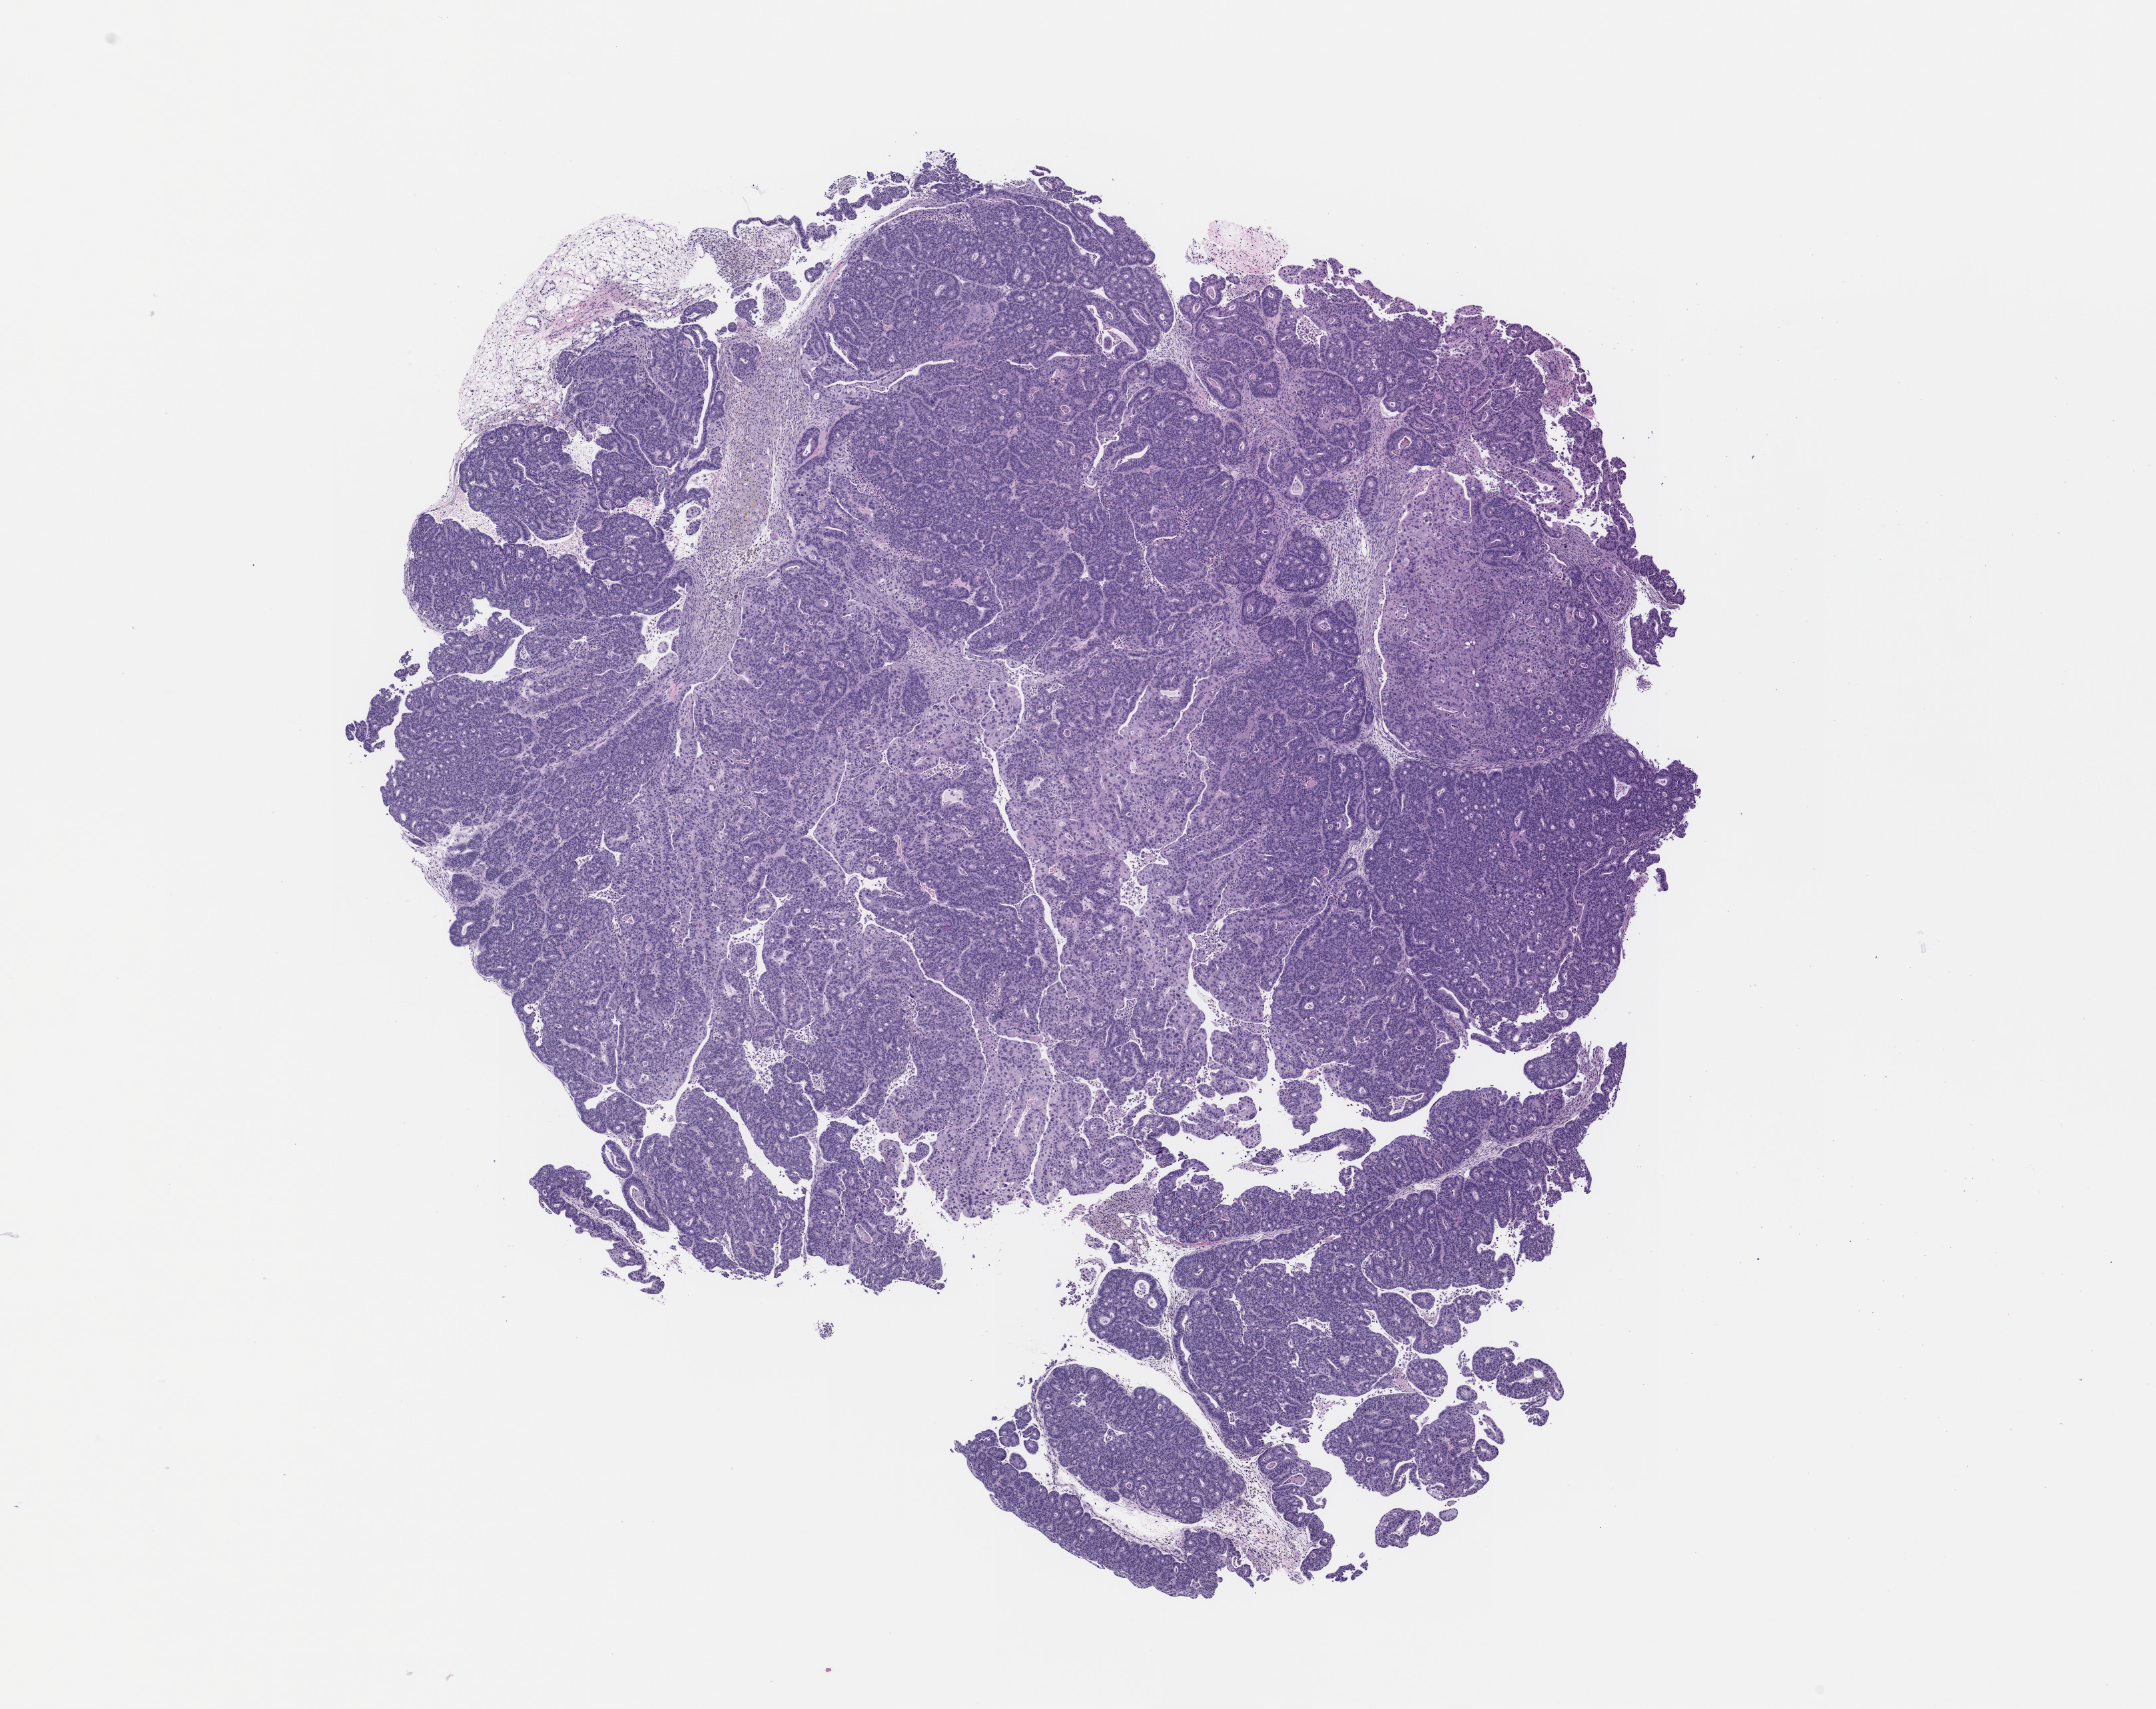
Whole-slide image, H&E: patient-derived xenograft (human tumor grown in a mouse), passage 2 — whole scanned area (about 13.0 x 10.3 mm) shown as a low-resolution overview. FFPE section. Tumor site category: colon.
Originating patient diagnosis: Colon Adenocarcinoma.